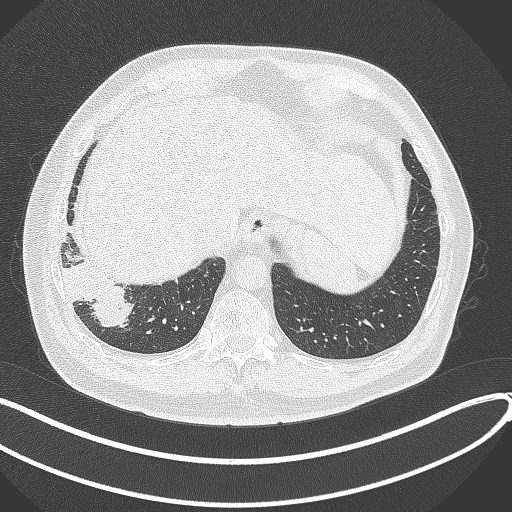
Chest CT, one axial slice; slice 61 of 360 in the series (ordered by position); 120 kVp; lung window (W 1500 / L -600 HU); 512 × 512 image matrix, field of view 400 × 400 mm. Patient: male, 59 years.
Structures marked on this image (rectangle marked by the reading radiologist):
- lung tumour (recorded histology: adenocarcinoma): box from (x=59, y=252) to (x=136, y=330) px